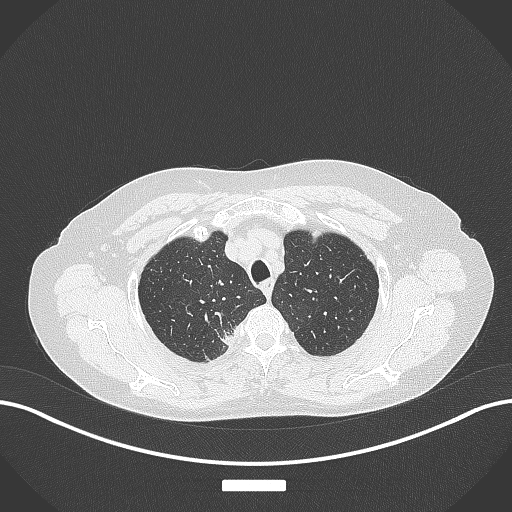
Chest CT, one axial slice. Slice 326 of 357 in the series (ordered by position). 120 kVp. Lung window (W 1500 / L -600 HU). 1 mm slice thickness. 512 × 512 image matrix, field of view 400 × 400 mm. Patient: female, 62 years. Case-level facts recorded for this patient, not image findings: clinical TNM (as recorded): T1c N1 M0.
Outlined on this slice (bounding box drawn by a radiologist):
- lung tumour (recorded histology: squamous cell carcinoma): box from (x=219, y=328) to (x=240, y=349) px